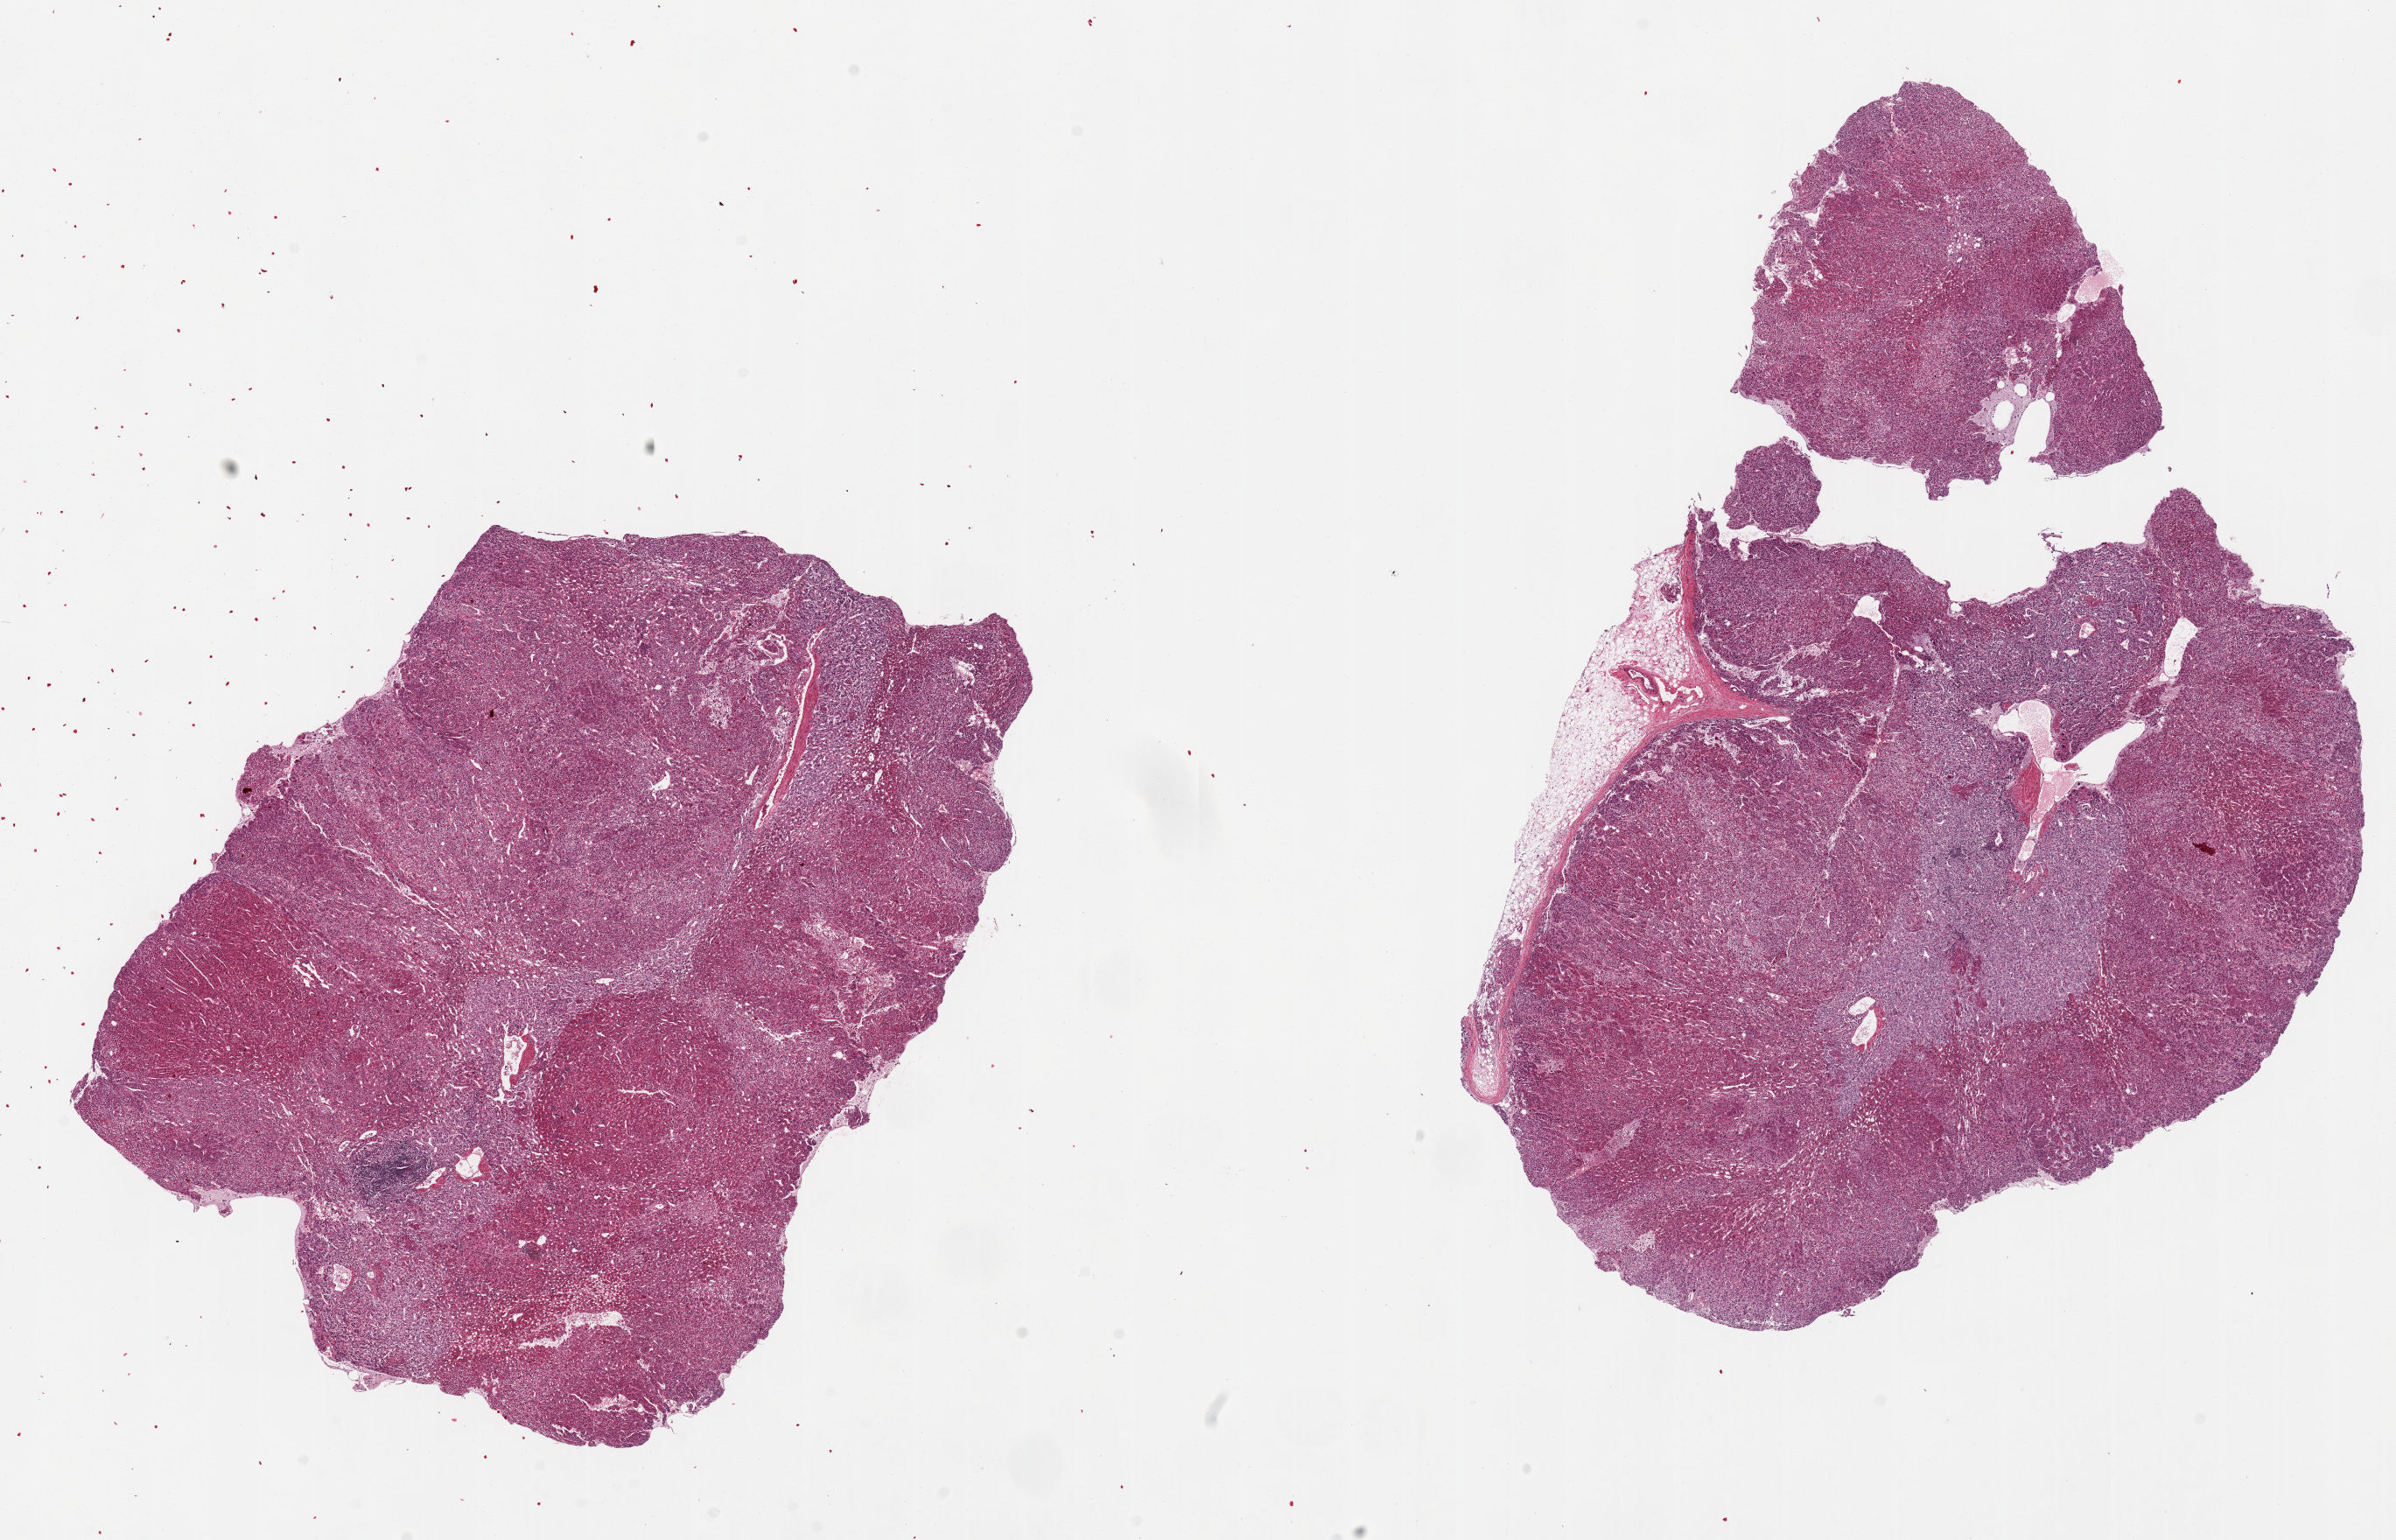
H&E whole-slide image — low-resolution overview of the scanned area, about 21.7 x 13.9 mm; PAXgene-fixed, paraffin-embedded tissue; sampled site (target tissue): adrenal gland; donor tissue sample. Donor sex: male.
- reviewer comment on this tissue sample: 2 pieces; cortex and medulla, small attachment of fat